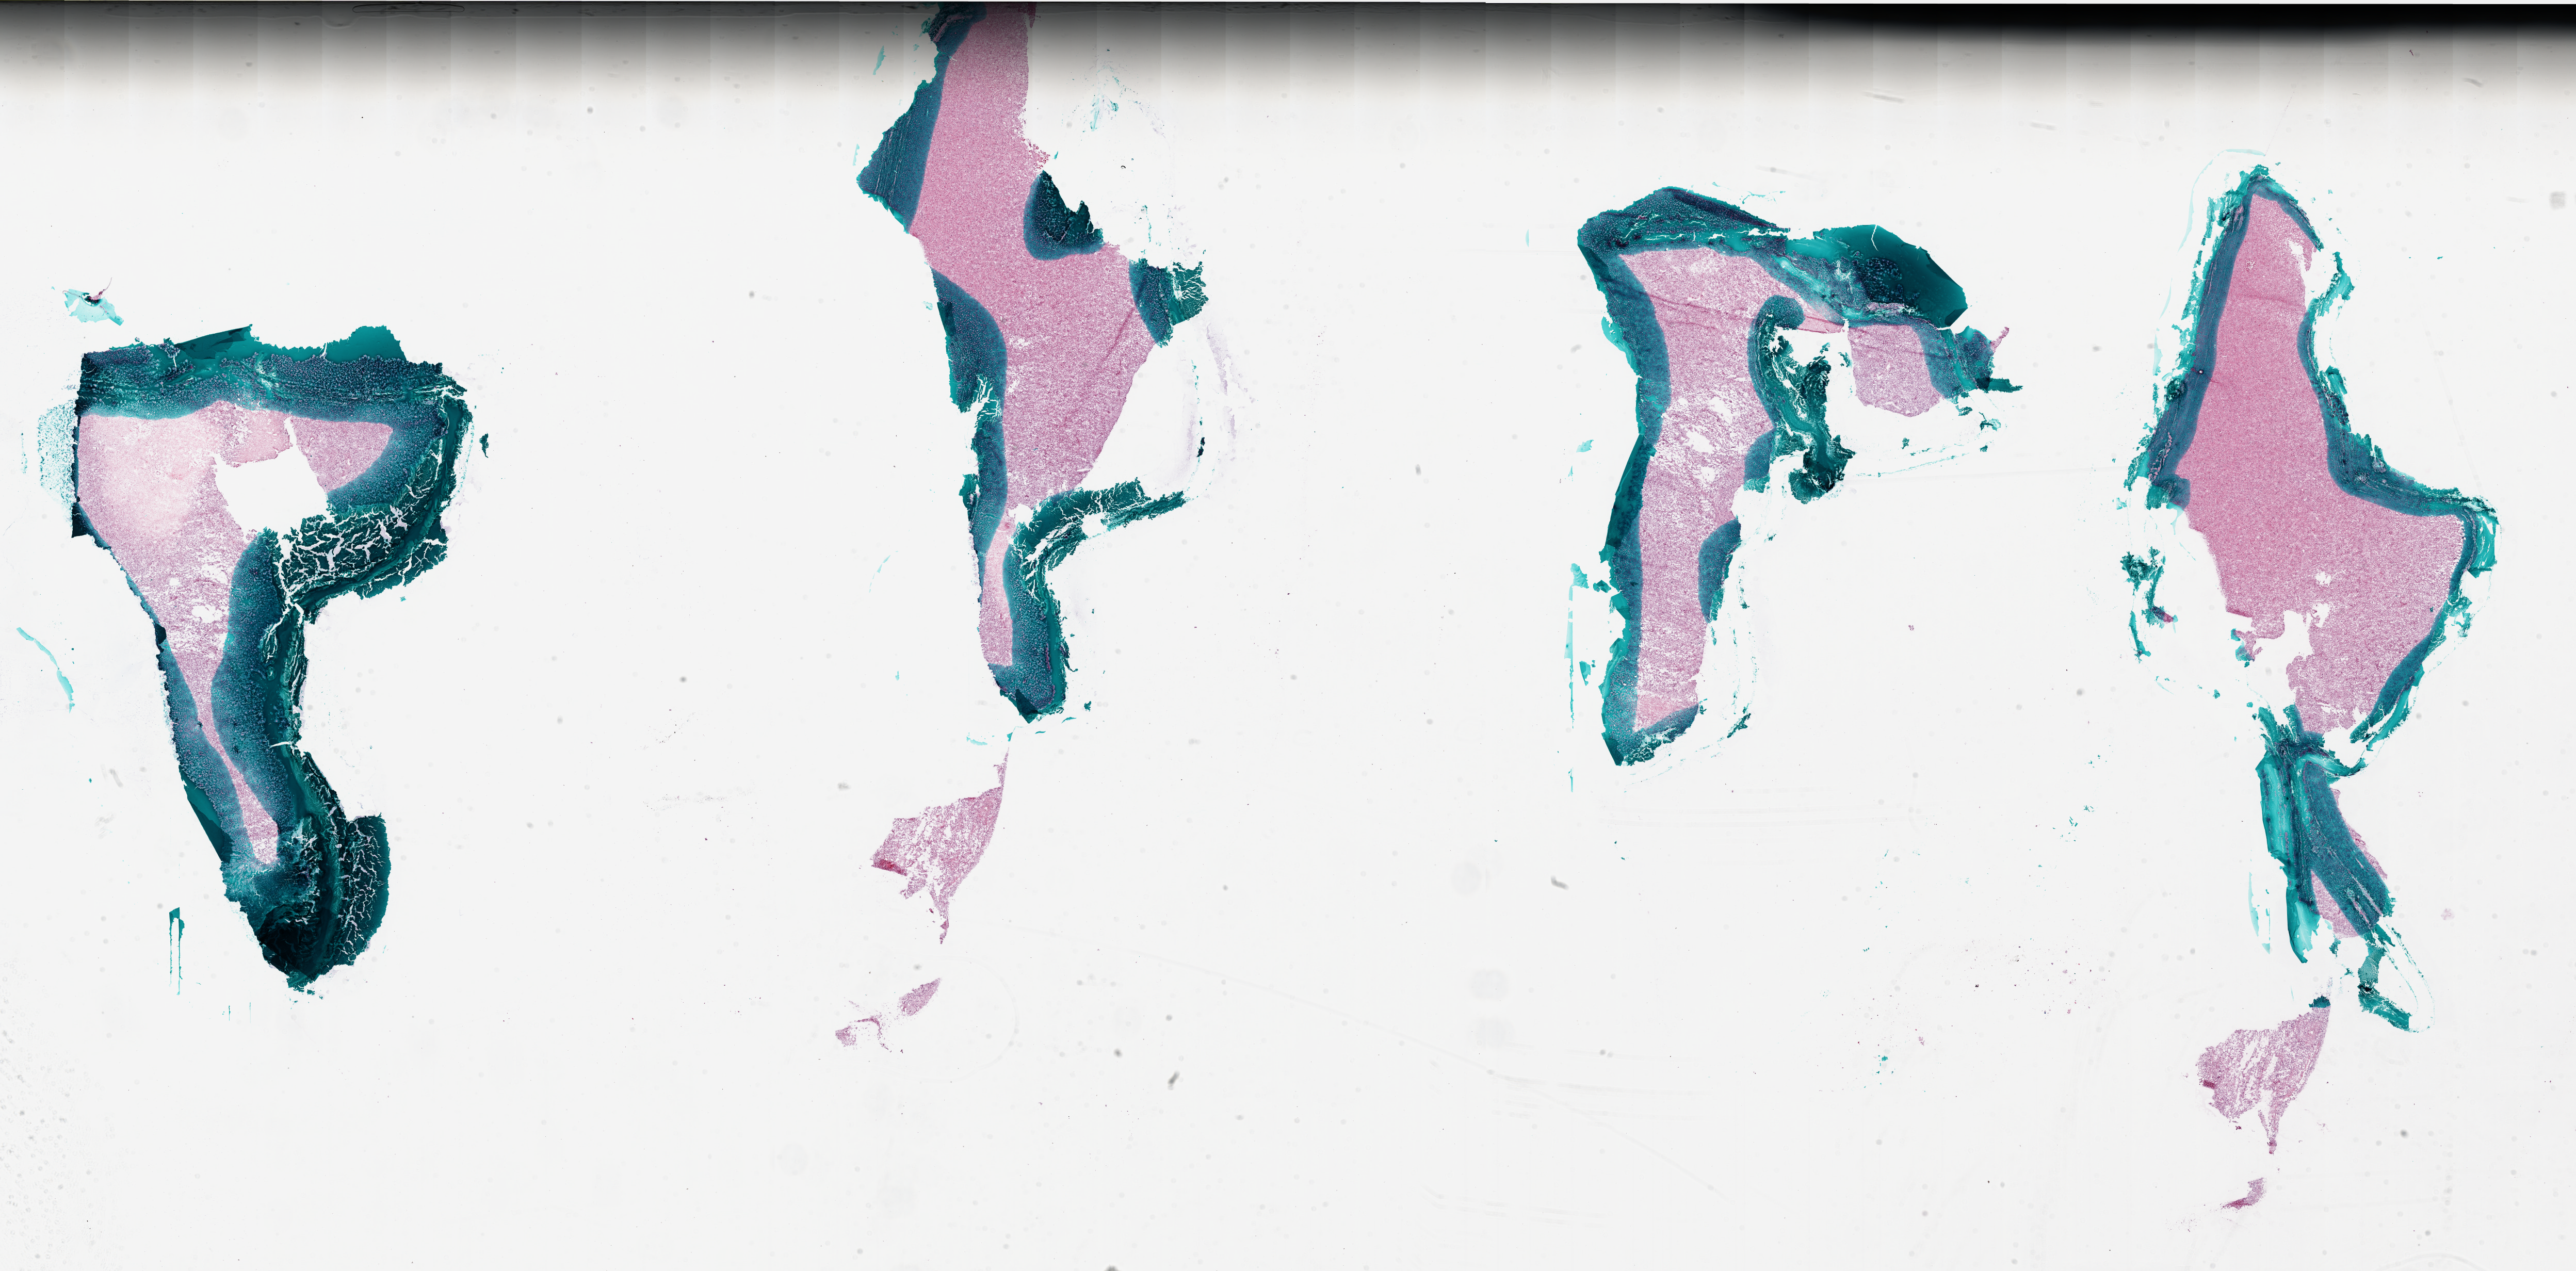
H&E-stained whole-slide image, low-resolution overview of the scanned area, about 40.0 x 19.7 mm (acquisition: 20x scan); frozen section from the bottom of the tissue portion; primary tumour sample from the brain. Male, age 52 years at initial diagnosis. Slide review estimates, as recorded: tumour cells 100%, tumour nuclei 100%, normal cells 0%, stromal cells 0%, necrosis 0%.
- pathologic diagnosis: Glioblastoma